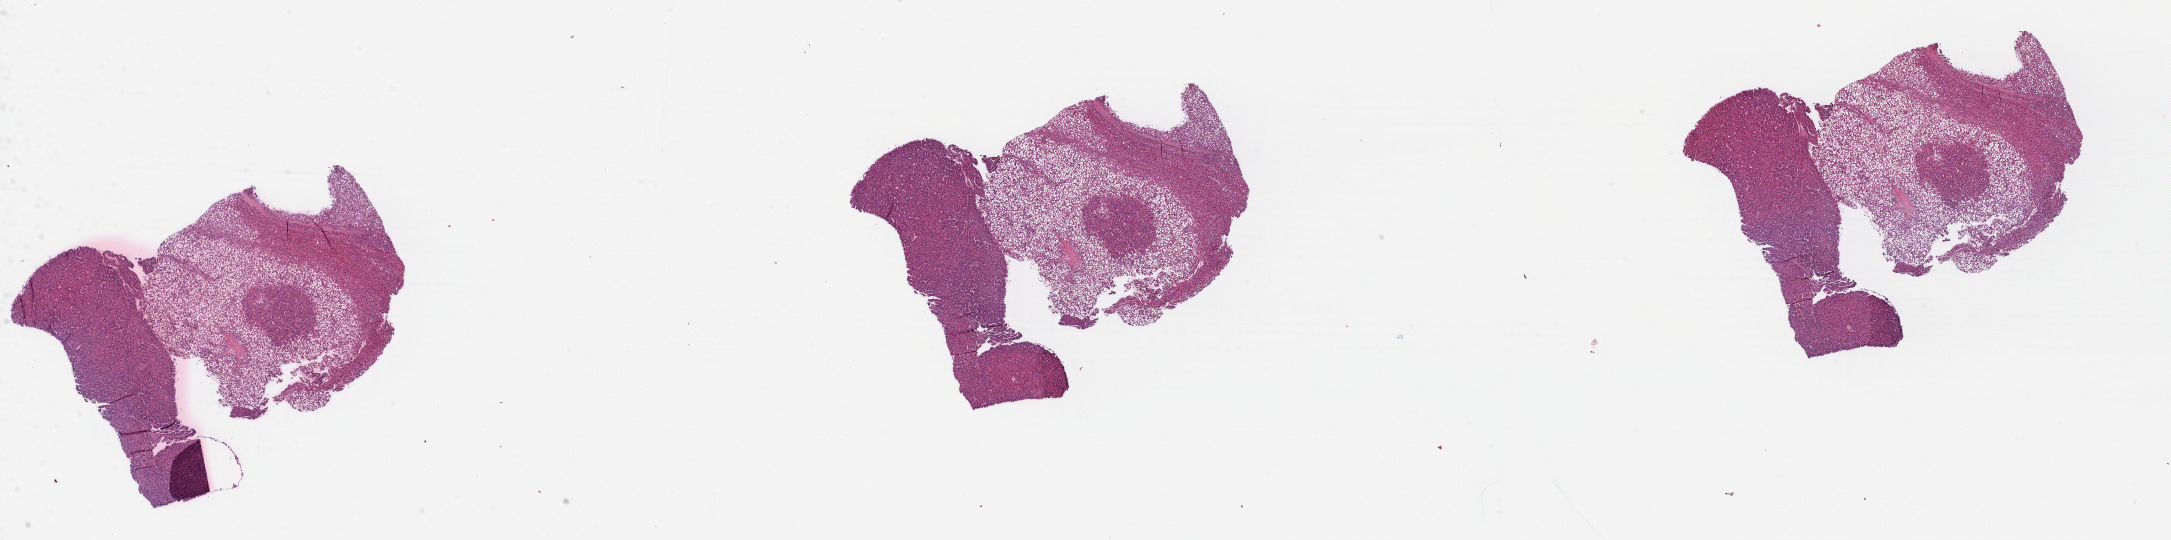
H&E whole-slide image — a low-resolution overview of the entire scanned area, about 34.1 x 8.5 mm; formalin-fixed paraffin-embedded (FFPE) diagnostic section; liver, primary tumour sample. Patient: male, age at initial diagnosis 62 years. Histologic grade: G3 (poorly differentiated).
* TNM: T1 NX MX
* diagnosis: Hepatocellular carcinoma, NOS
* AJCC pathologic stage: I (7th edition)